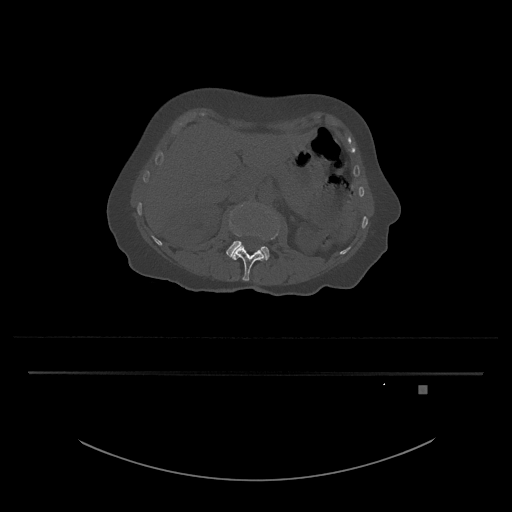
CT including the spine, one axial slice; slice 468 of 797 in the series (ordered by position); 120 kVp; bone window (W 1800 / L 400 HU); 0.5 mm slice thickness; 512 × 512 image matrix, field of view 500 × 500 mm. Female patient, age 57 years. From the clinical record (not read from this slice): primary cancer: cervical.
Annotated regions visible in this slice (semi-automatic segmentation, software-assisted and operator-edited):
- L3 vertebra: box from (x=226, y=205) to (x=279, y=260) px